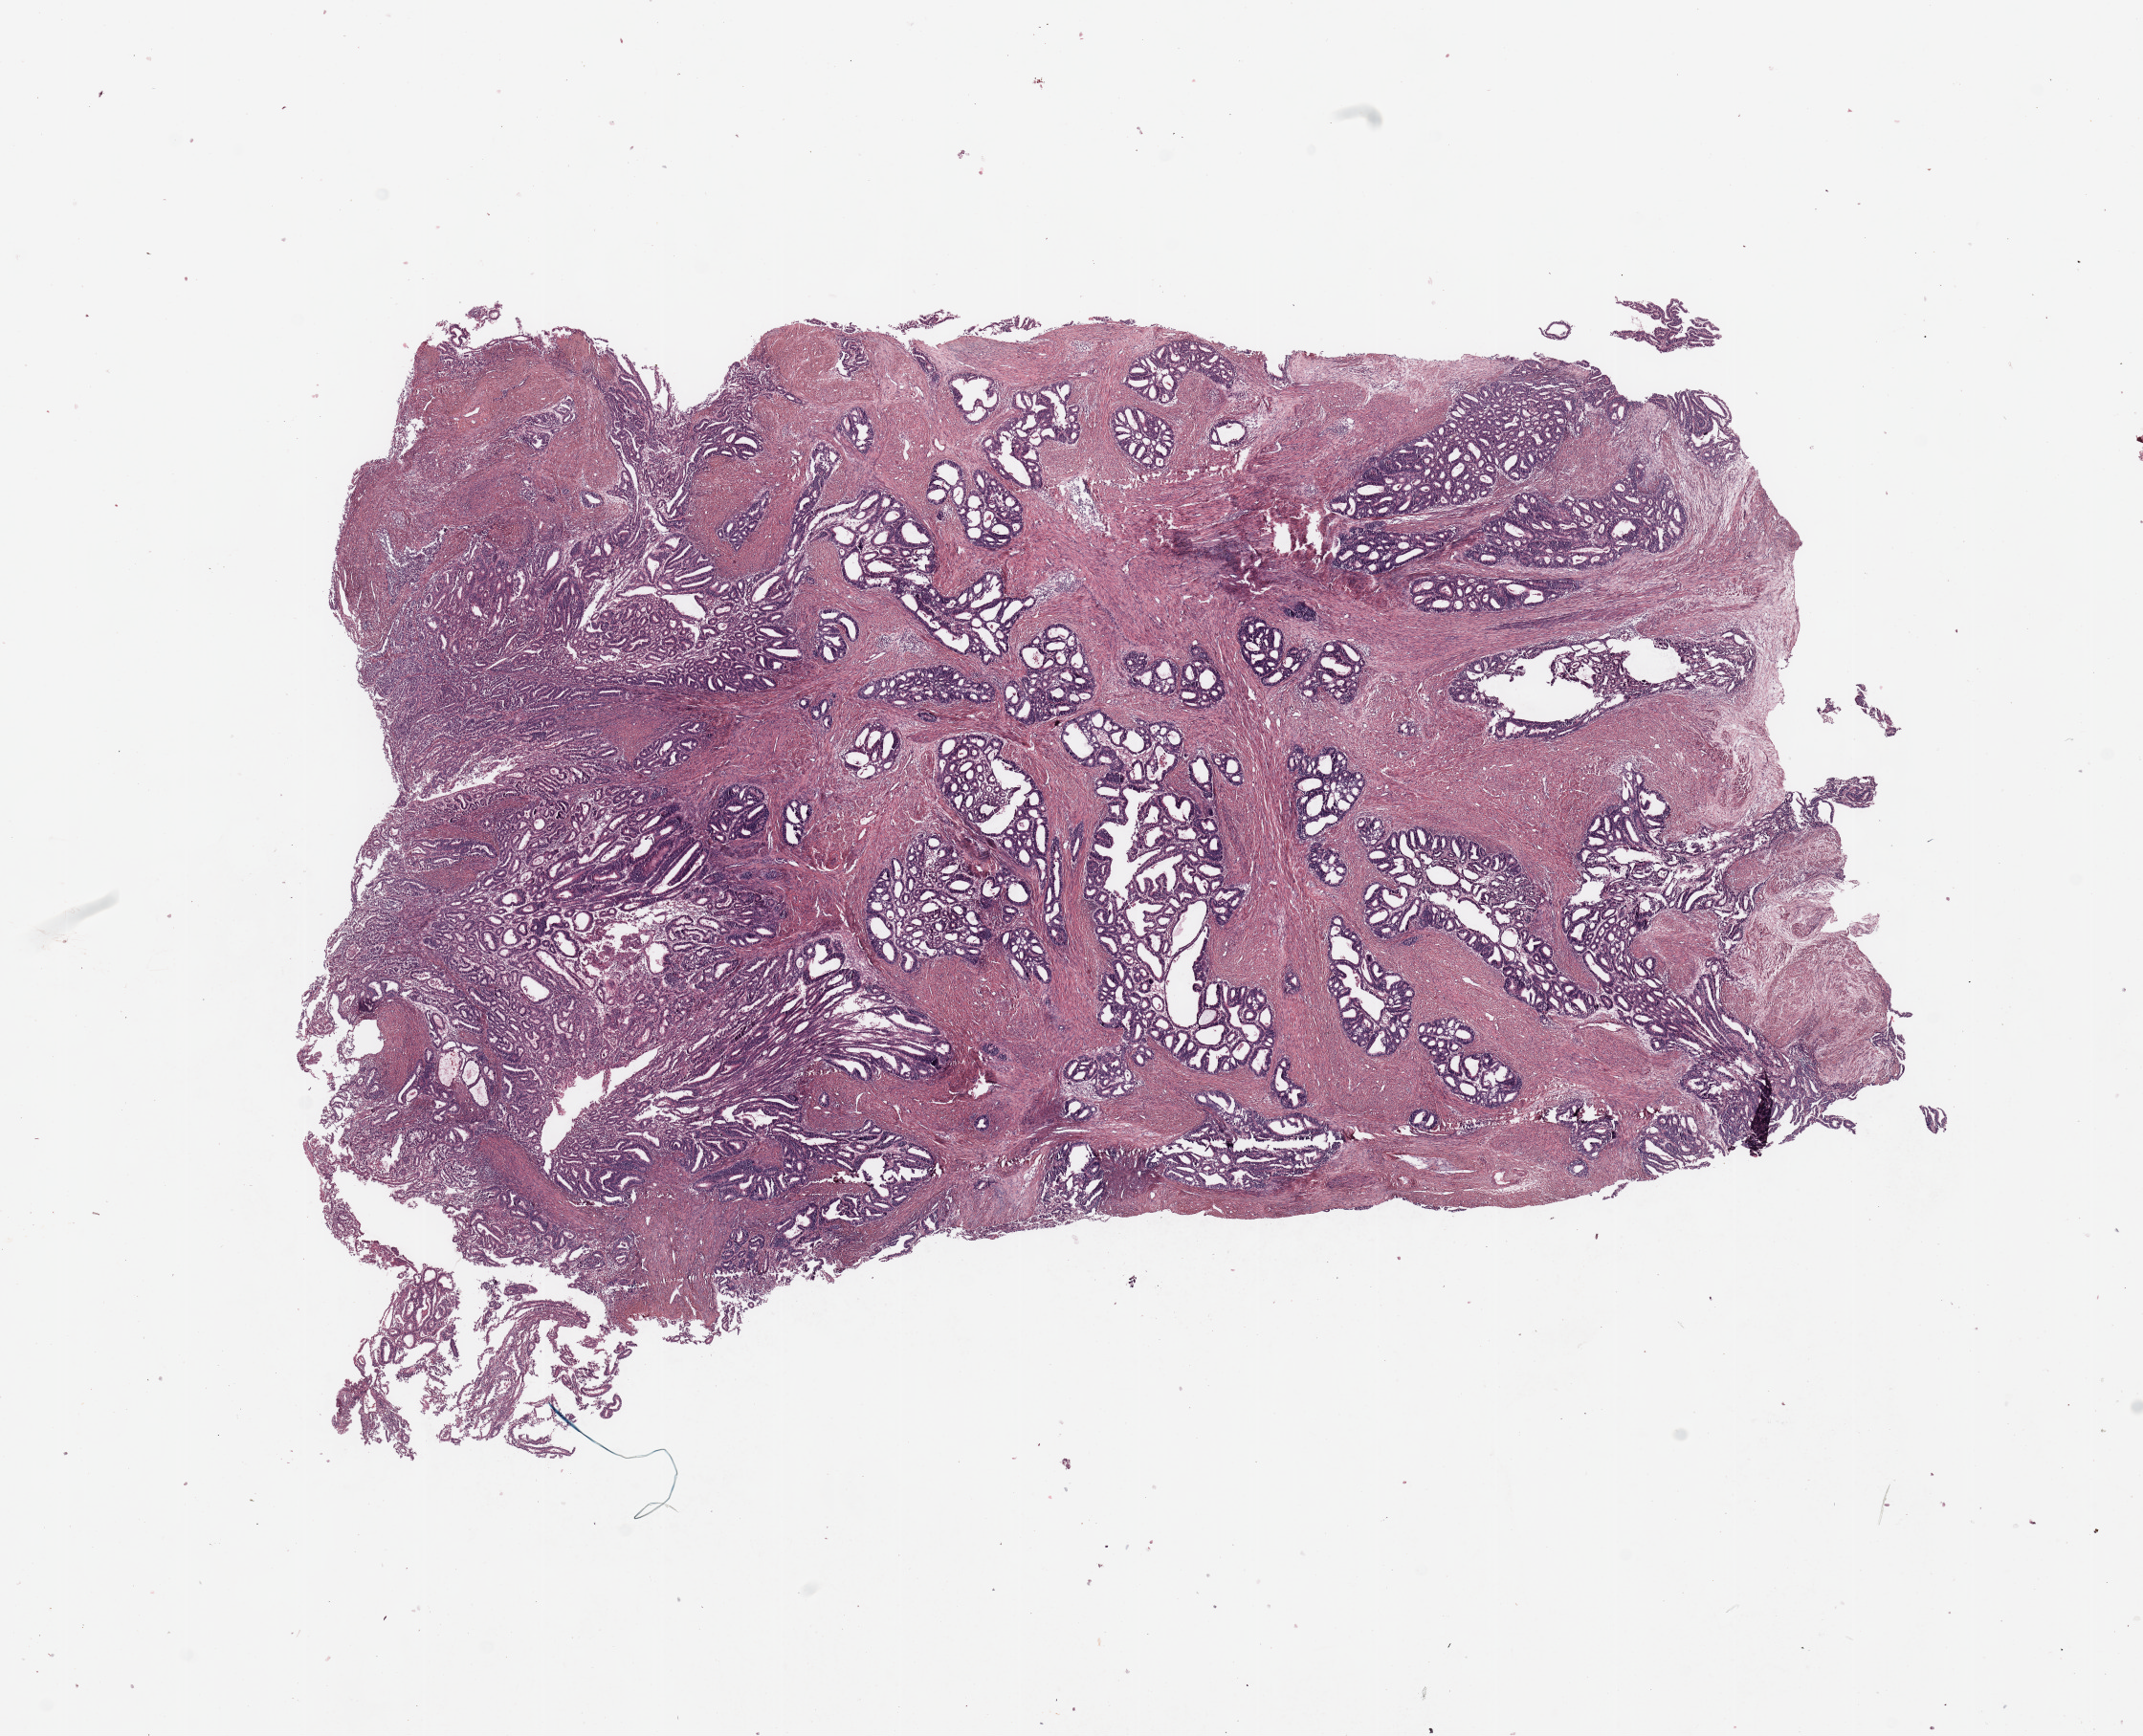
Digitized H&E tissue section (whole slide) — shown as a low-resolution overview of the whole scanned area (about 17.7 x 14.4 mm, acquisition: 20x scan). Tumour tissue sample, sampled site: uterus. Patient: female, age 67 years. Histologic grade: G2 (moderately differentiated). Slide review estimates, as recorded: tumour nuclei 80%, necrosis 0%.
AJCC pathologic stage: I. Diagnosis: Endometrioid adenocarcinoma, NOS.